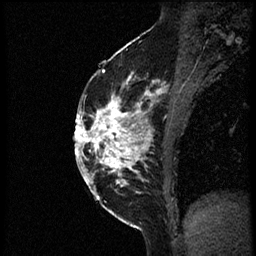
Breast MRI (dynamic contrast-enhanced), one sagittal slice; slice 33 of 56 in the series (ordered by position); dynamic contrast-enhanced study with each time point stored as its own series, time point 2 of 3 at this slice position (early post-contrast, ordered by acquisition time); 1.5 T; TE 4.2 ms, TR 21.3 ms; 2 mm slice thickness; 256 × 256 image matrix, field of view 200 × 200 mm. Patient: female, 41 years. Case-level facts recorded for this patient, not image findings: setting: breast cancer imaged before/during neoadjuvant chemotherapy; receptor status: HER2-positive.
Structures marked on this image (semi-automatic segmentation, software-assisted and operator-edited):
- analysis volume of interest (the breast-tissue region the enhancement analysis was run in; not a lesion): bounding box <85,73,177,205> (left, top, right, bottom; pixels)
- tumour enhancement mask (voxels above the 100 % enhancement threshold inside the analysis volume of interest): <85,79,163,197>